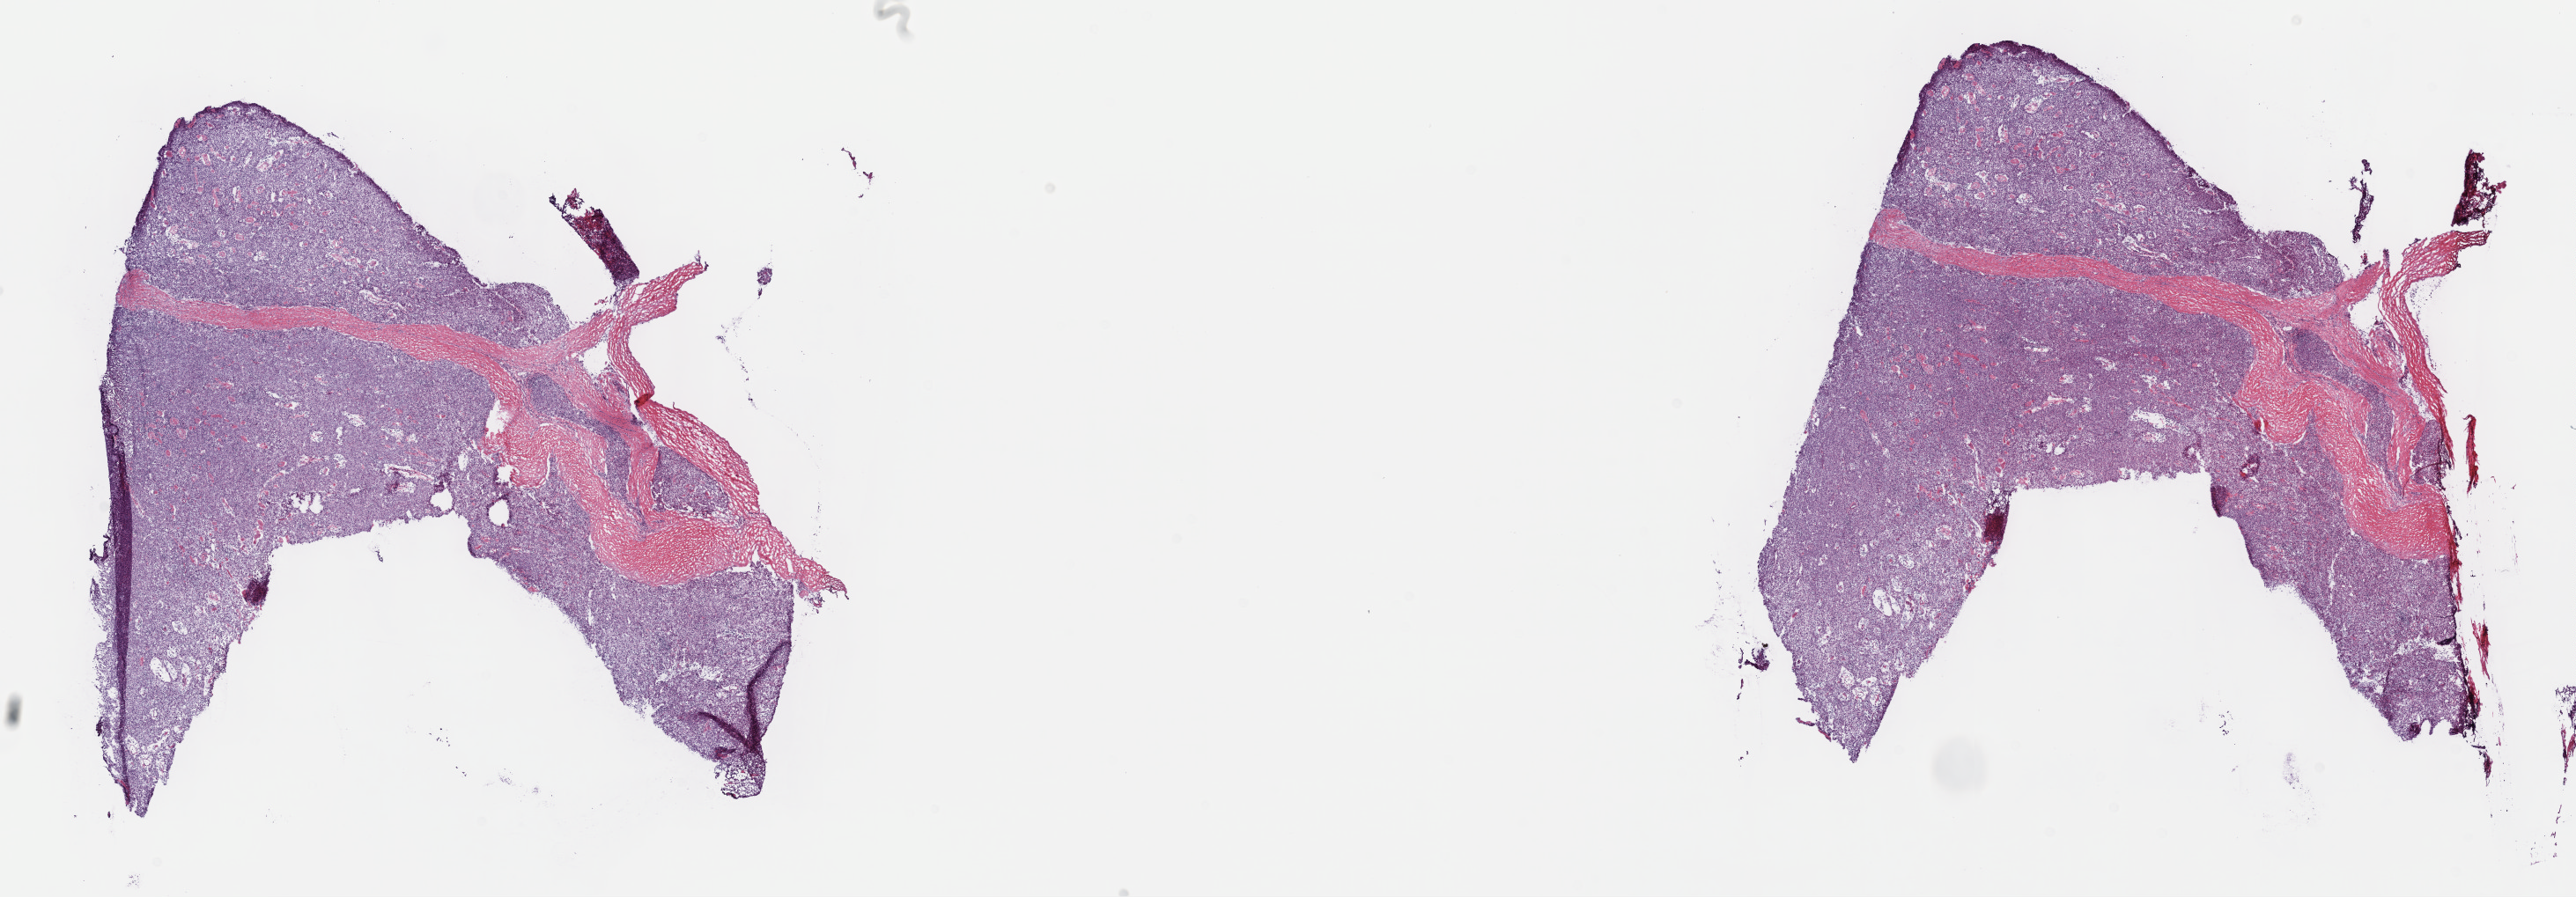
Whole-slide histology image, H&E-stained — low-resolution overview of the scanned area, about 23.7 x 8.2 mm. Frozen section from the top of the tissue portion. Thymus, primary tumour sample. Female patient; age at initial diagnosis 71 years. Slide review estimates, as recorded: tumour cells 85%, tumour nuclei 97%, normal cells 0%, stromal cells 15%, necrosis 0%. Infiltration values recorded for this section: lymphocyte infiltration 0%, monocyte infiltration 0%, neutrophil infiltration 0%.
Pathologic diagnosis: Thymoma, type AB, malignant (anterior mediastinum).